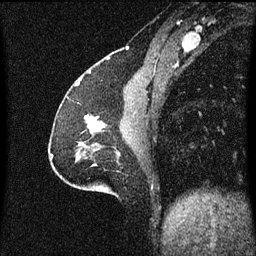
Breast MRI (dynamic contrast-enhanced), one sagittal slice. Slice 23 of 60 in the series (ordered by position). Dynamic contrast-enhanced series, image 2 of 3 at this slice position (ordered by acquisition). 1.5 T. TE 4.2 ms, TR 8.4 ms. 2 mm slice thickness. 256 × 256 image matrix, field of view 200 × 200 mm. Patient: female, 51 years.
Structures marked on this image (semi-automatically segmented with operator editing):
- analysis volume of interest (the breast-tissue region the enhancement analysis was run in; not a lesion): box from (x=84, y=116) to (x=106, y=139) px
- tumour enhancement mask (voxels above the 70 % enhancement threshold inside the analysis volume of interest): (x=84, y=116)–(x=104, y=133)